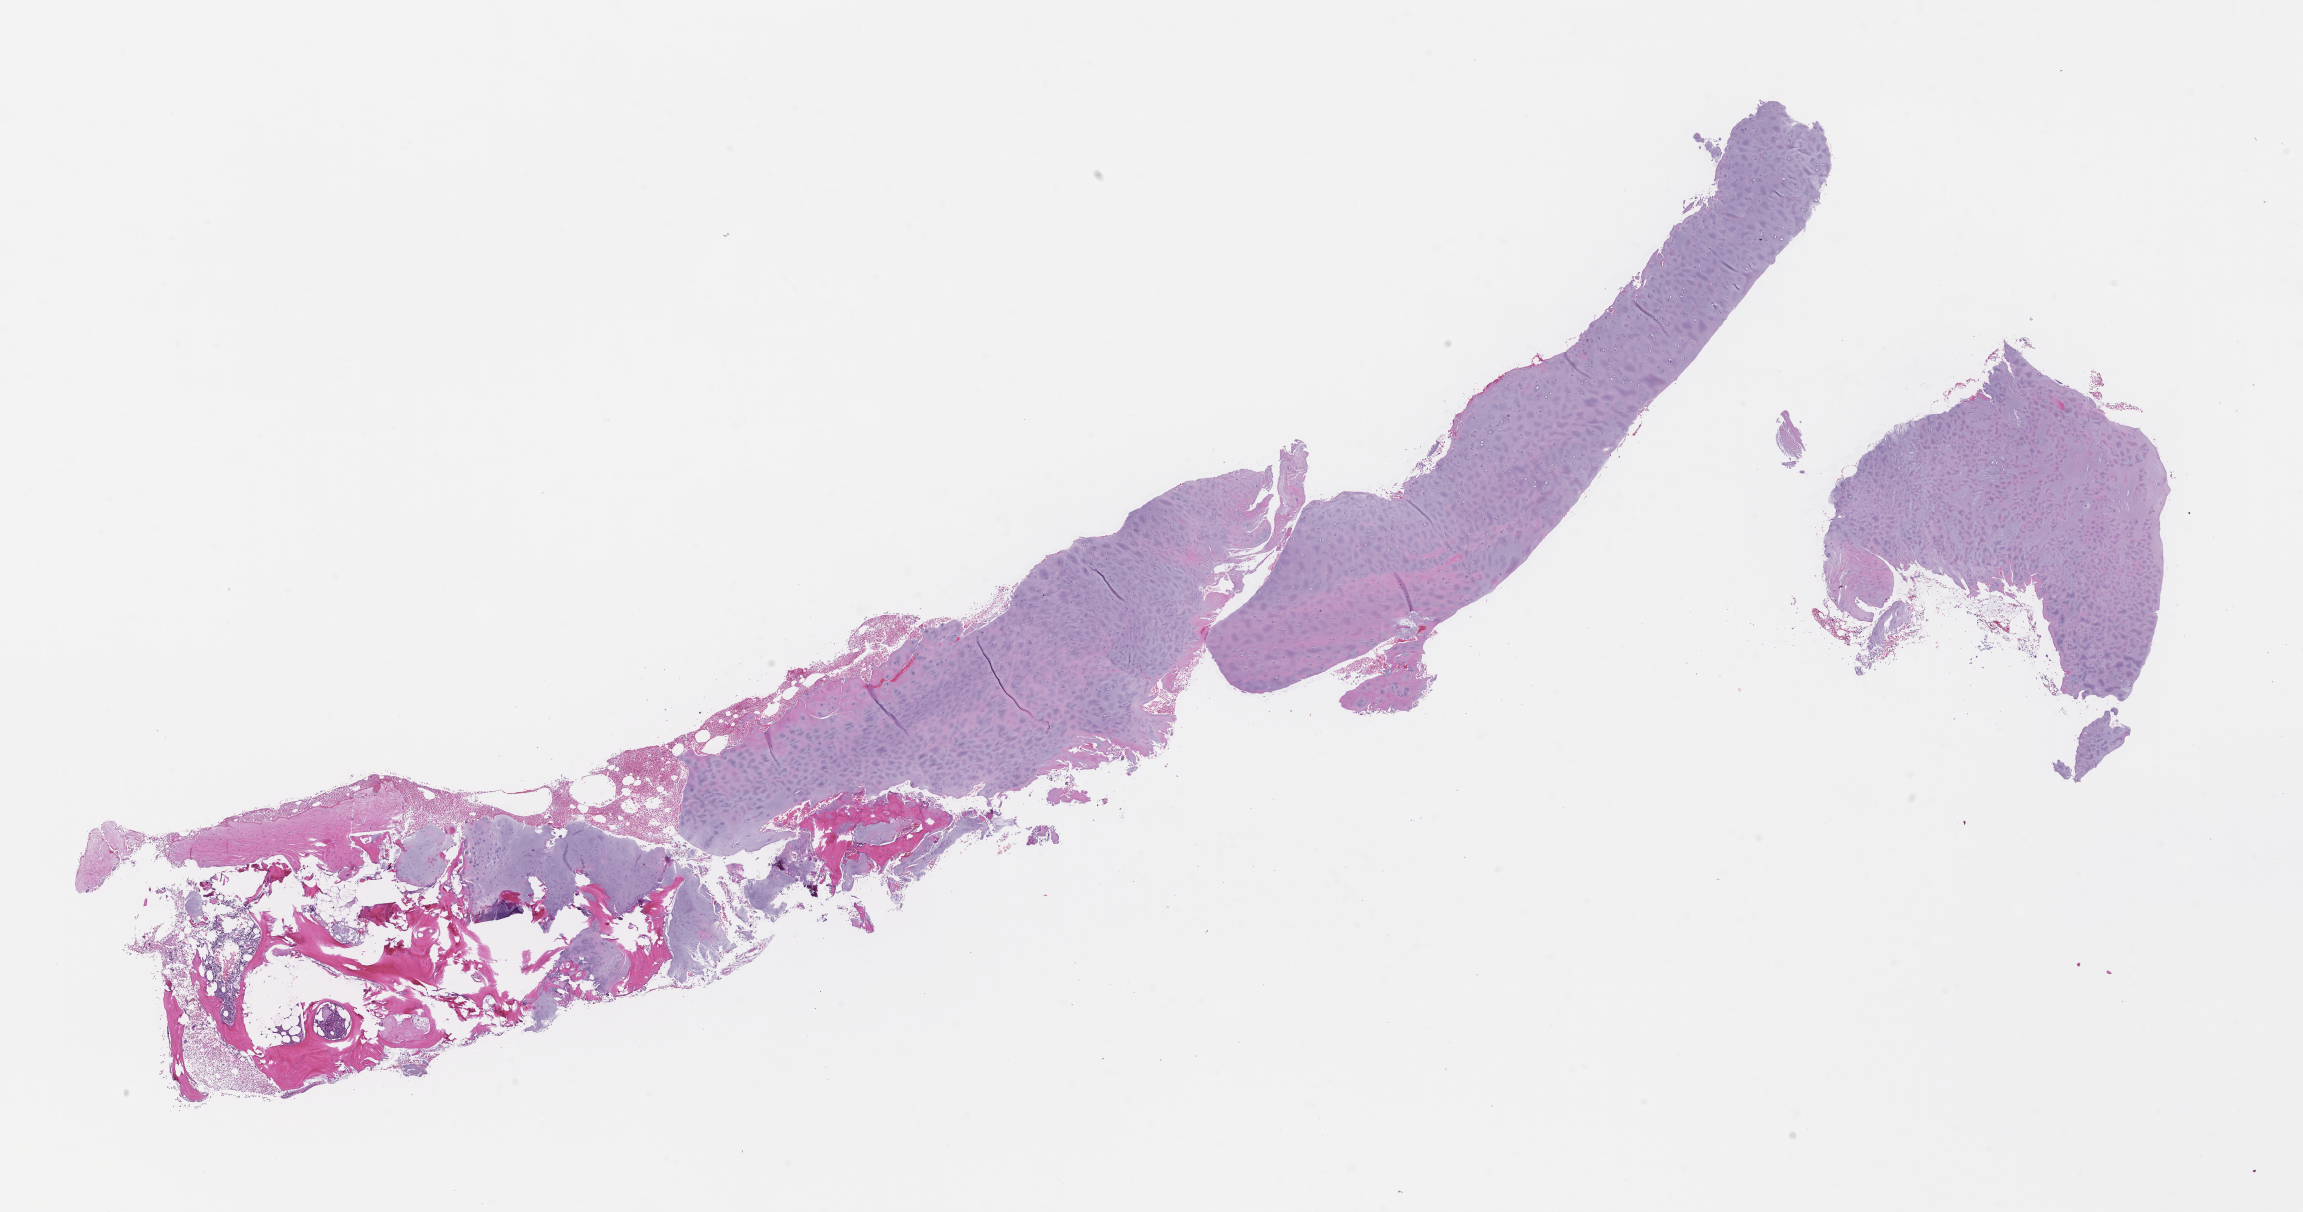
H&E whole-slide image — a low-resolution overview of the entire scanned area, about 18.6 x 9.8 mm, formalin-fixed paraffin-embedded section, site: bone marrow, collected at baseline (before treatment). Patient sex: female.
This section: primary tumor. Diagnosis: Plasma Cell Myeloma.